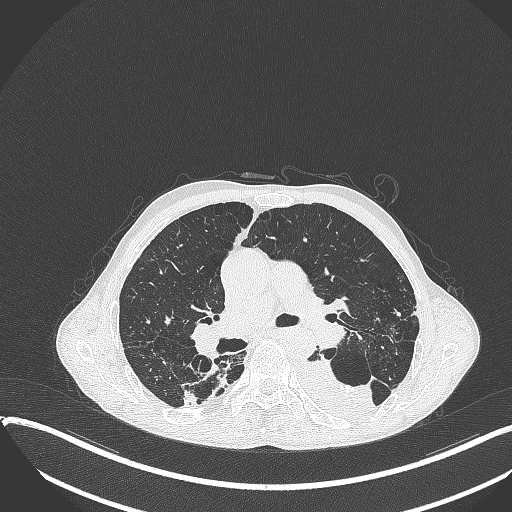
Chest CT, one axial slice. Position 230 of 401 along the scan axis. Reconstruction kernel B70f. 120 kVp. Lung window (W 1500 / L -600 HU). 512 × 512 image matrix, field of view 400 × 400 mm. Male patient, age 57 years. Case-level facts recorded for this patient, not image findings: clinical TNM (as recorded): T4 N0 M0.
Structures marked on this image (rectangle marked by the reading radiologist):
- lung tumour (recorded histology: squamous cell carcinoma): bounding box <295,354,380,424> (left, top, right, bottom; pixels)